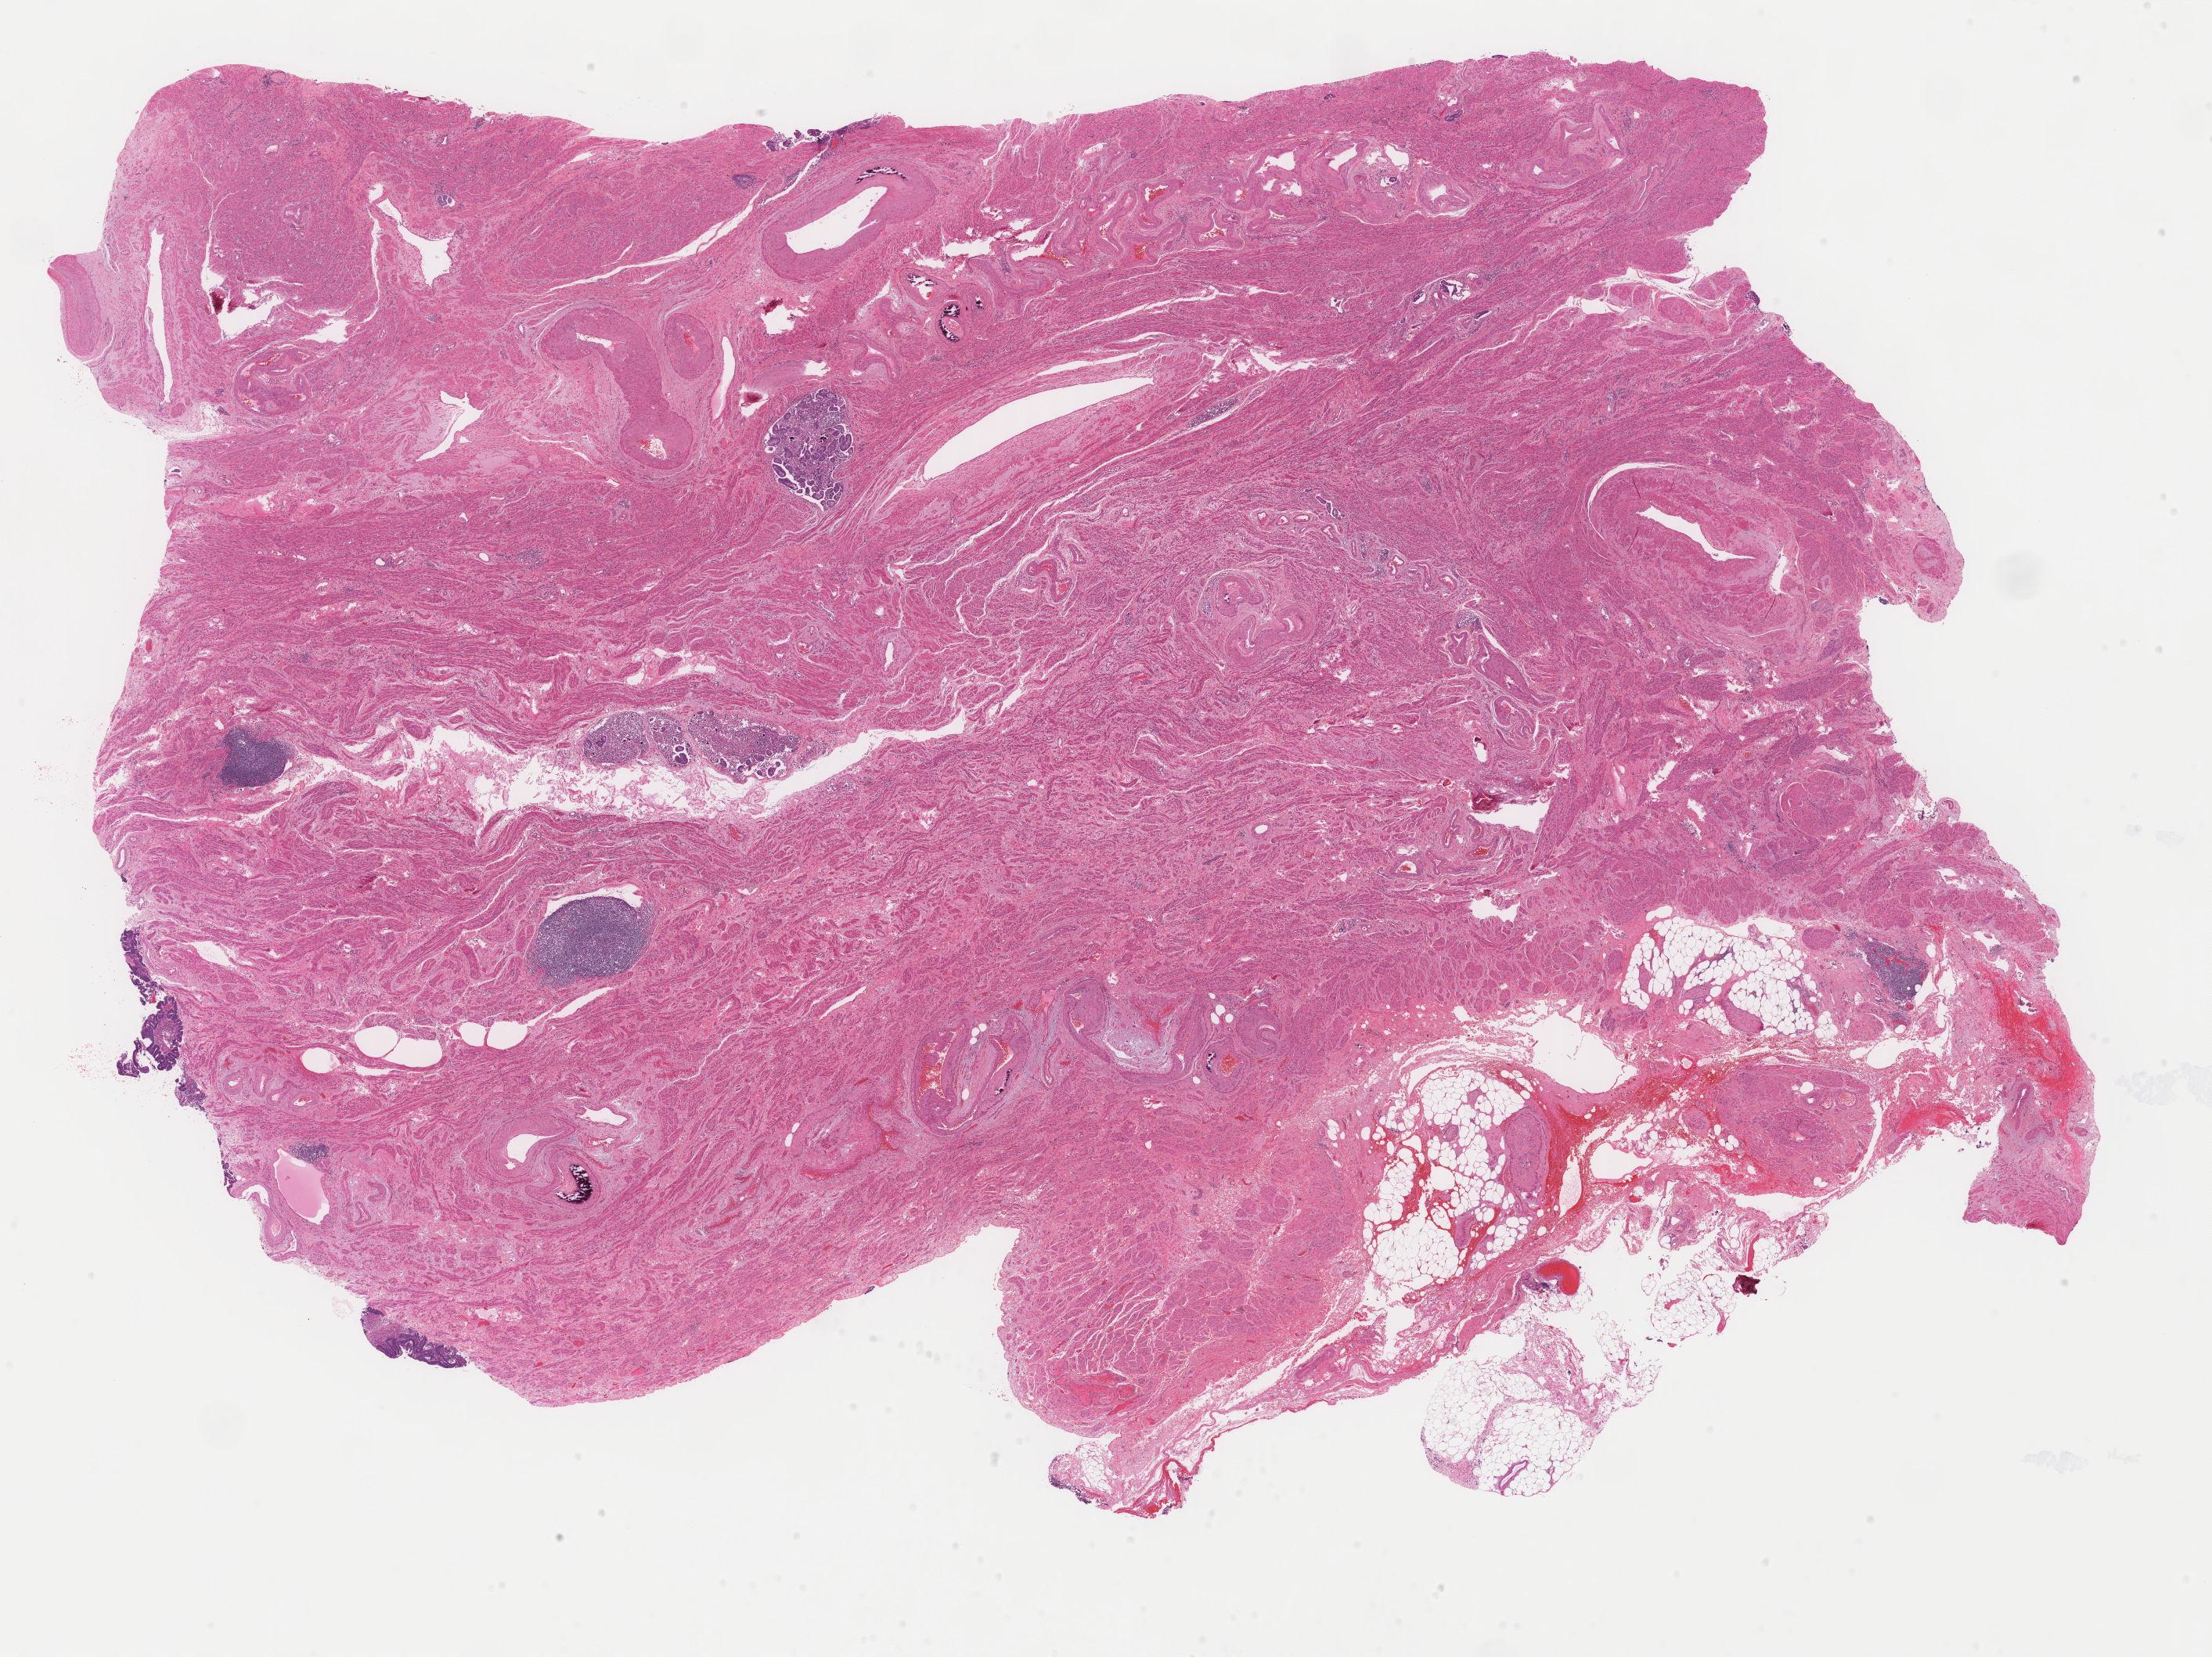
Digitized H&E tissue section (whole slide), whole scanned area (about 22.4 x 16.8 mm, acquisition: 40x scan) shown as a low-resolution overview, formalin-fixed paraffin-embedded (FFPE) diagnostic section, primary tumour sample from the uterus. Patient: female, age at initial diagnosis 83 years.
FIGO stage: IB. Diagnosis: Mullerian mixed tumor (fundus uteri).